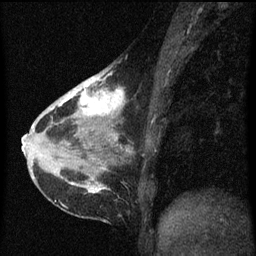
Breast MRI (dynamic contrast-enhanced), one sagittal slice. Dynamic contrast-enhanced series, image 2 of 3 at this slice position (ordered by acquisition). 1.5 T. TE 4.2 ms, TR 8 ms. 2 mm slice thickness. 256 × 256 image matrix, field of view 180 × 180 mm. Female patient, age 38 years.
Outlined on this slice (semi-automatically segmented with operator editing):
- analysis volume of interest (the breast-tissue region the enhancement analysis was run in; not a lesion): bounding box <61,66,127,147> (left, top, right, bottom; pixels)
- tumour enhancement mask (voxels above the 70 % enhancement threshold inside the analysis volume of interest): <61,72,124,139>